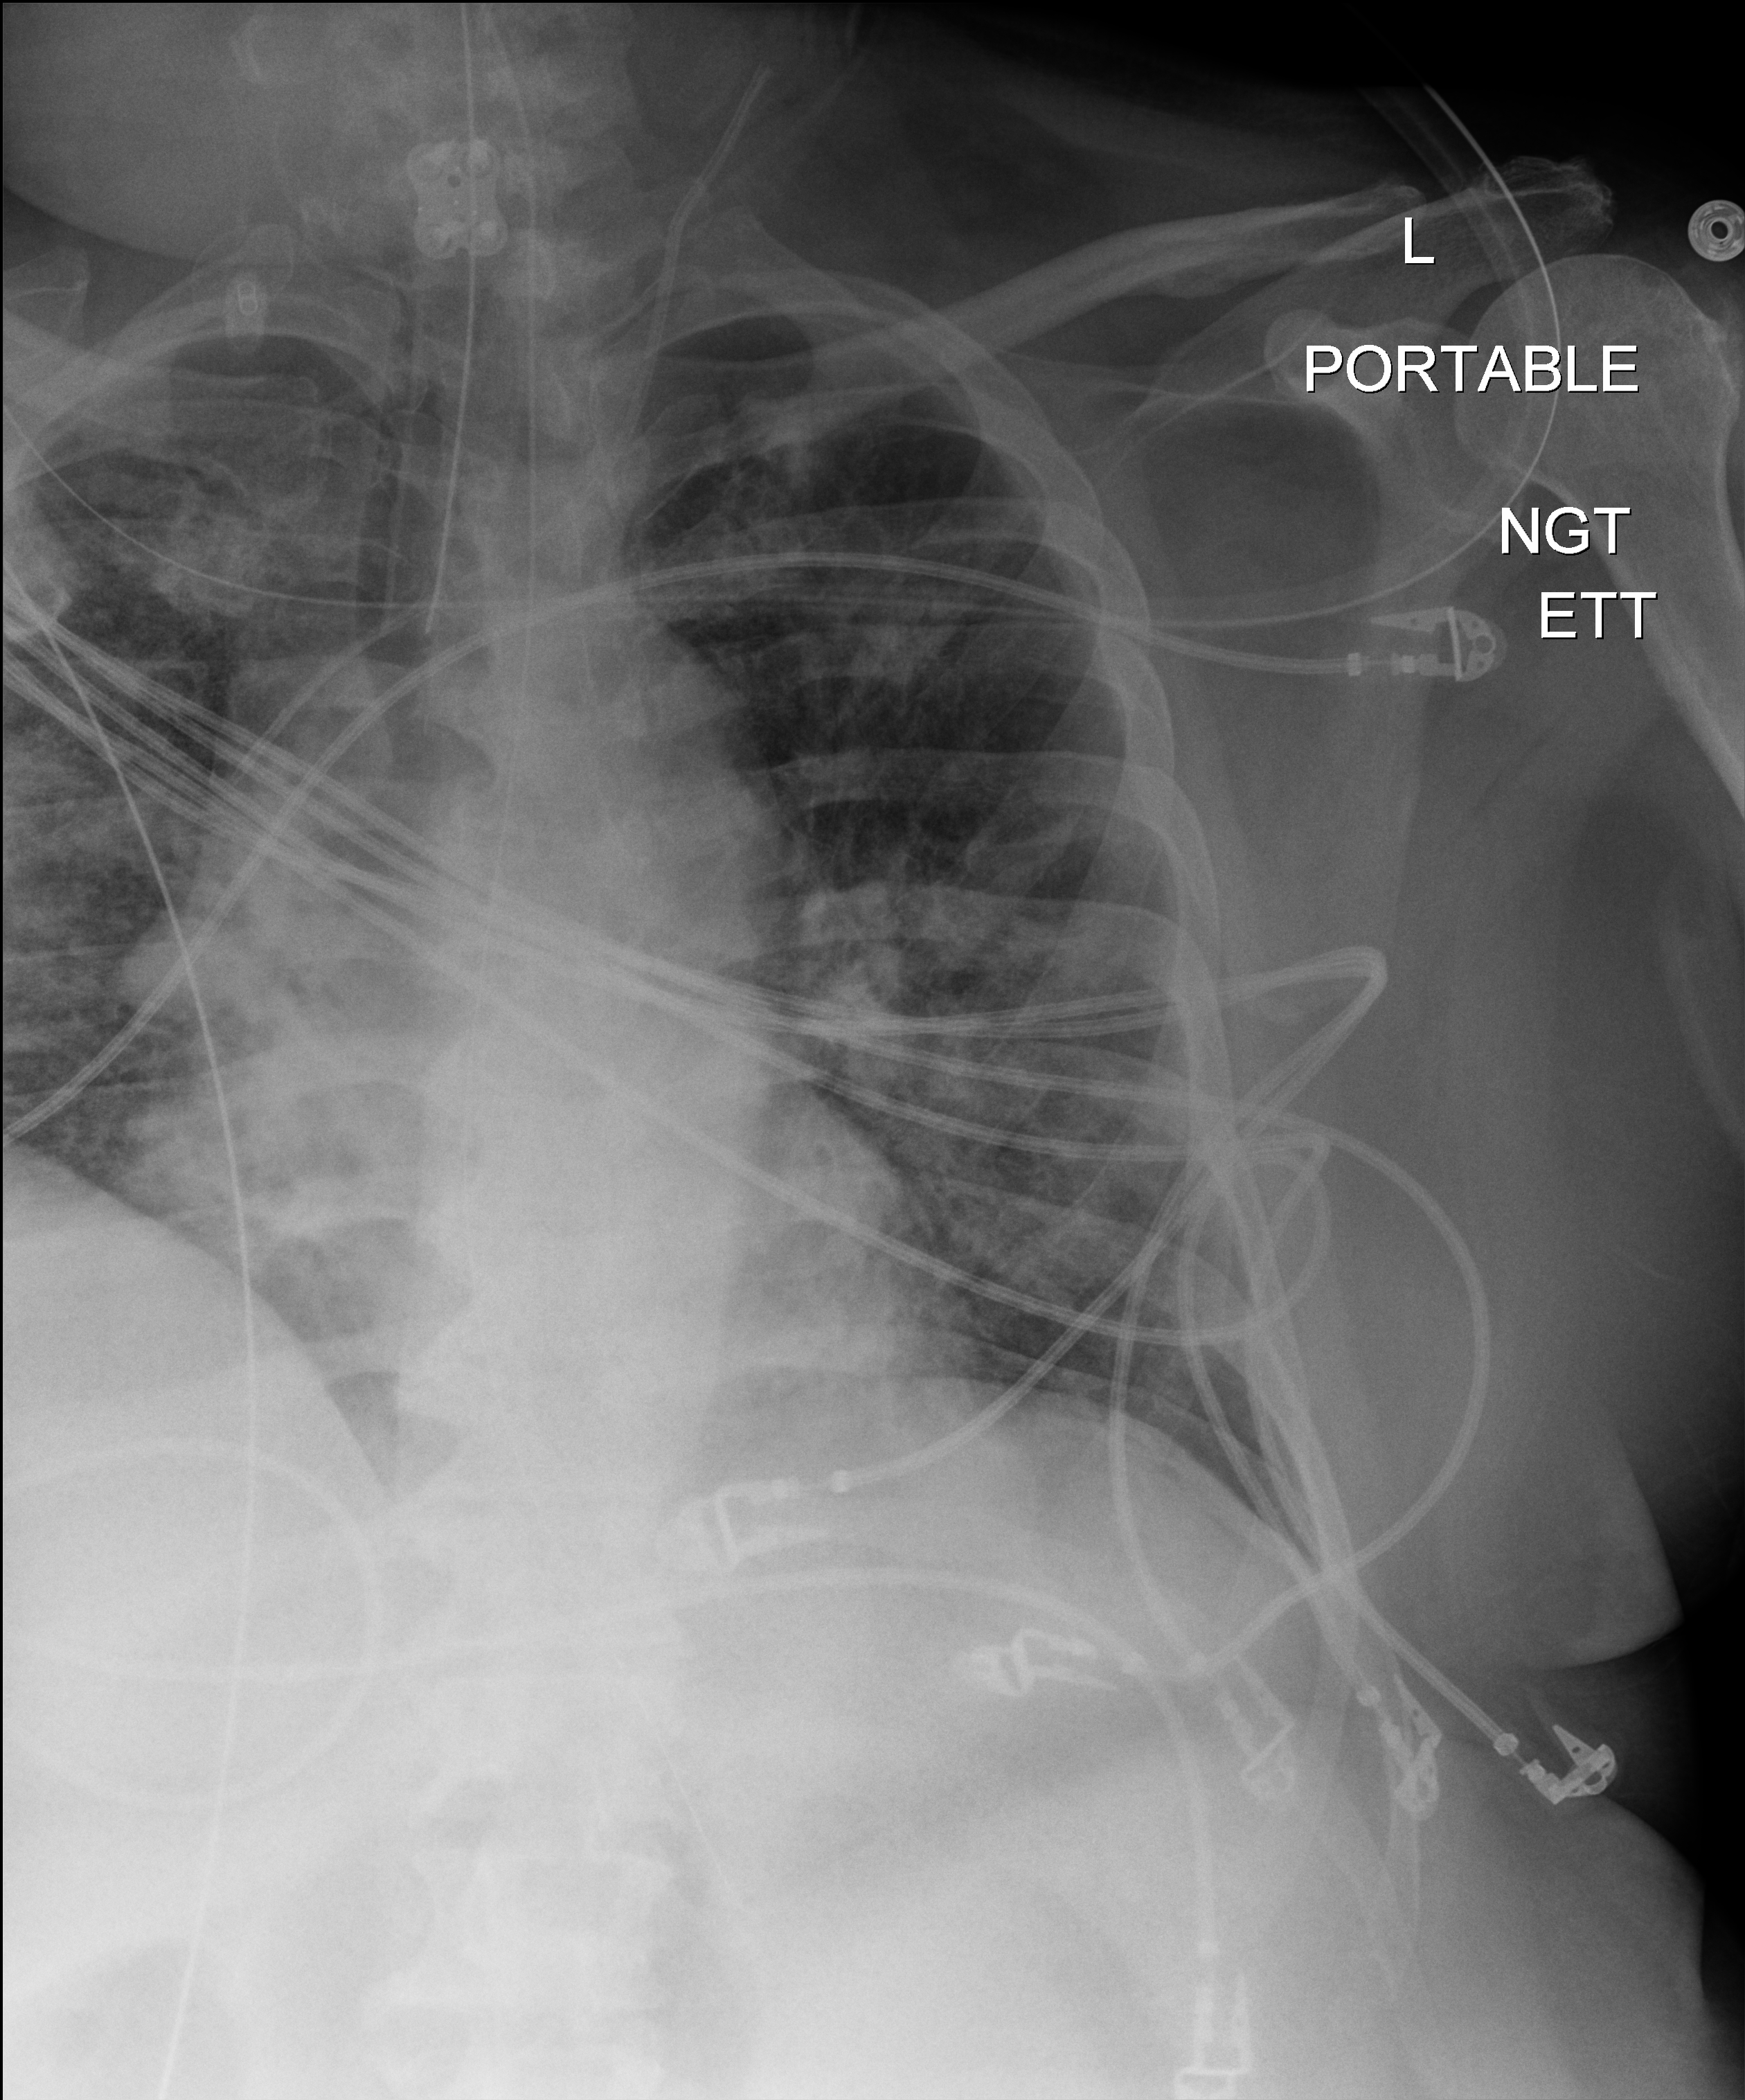
Chest X-ray (portable), anteroposterior (AP) projection. Male patient hospitalised with COVID-19, age 18–59 years.
From the hospital-stay record, not from the radiograph (when in the stay this image was taken is not recorded): admitted to intensive care during this hospital stay: yes.